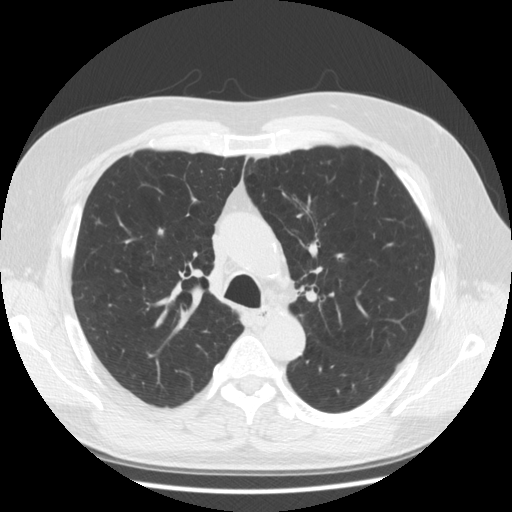
Axial slice from a low-dose chest CT screening exam. Second screening round (one year after baseline). Lung window (W 1500 / L -600 HU). Standard (soft-tissue) reconstruction kernel (STANDARD). Slice 57 of 173 in the series. 512 × 512 image matrix, field of view 360 × 360 mm. Male participant, aged 63 years at enrolment.
Lesion marked by an expert reader, bounding box <144,219,177,244> (left, top, right, bottom; pixels). No non-calcified nodule or mass ≥4 mm was recorded by the screening reader at this exam. Lung cancer was diagnosed 717 days after this screen: adenocarcinoma, NOS, right upper lobe, stage IIA (AJCC 6th edition), 8 mm at pathology.